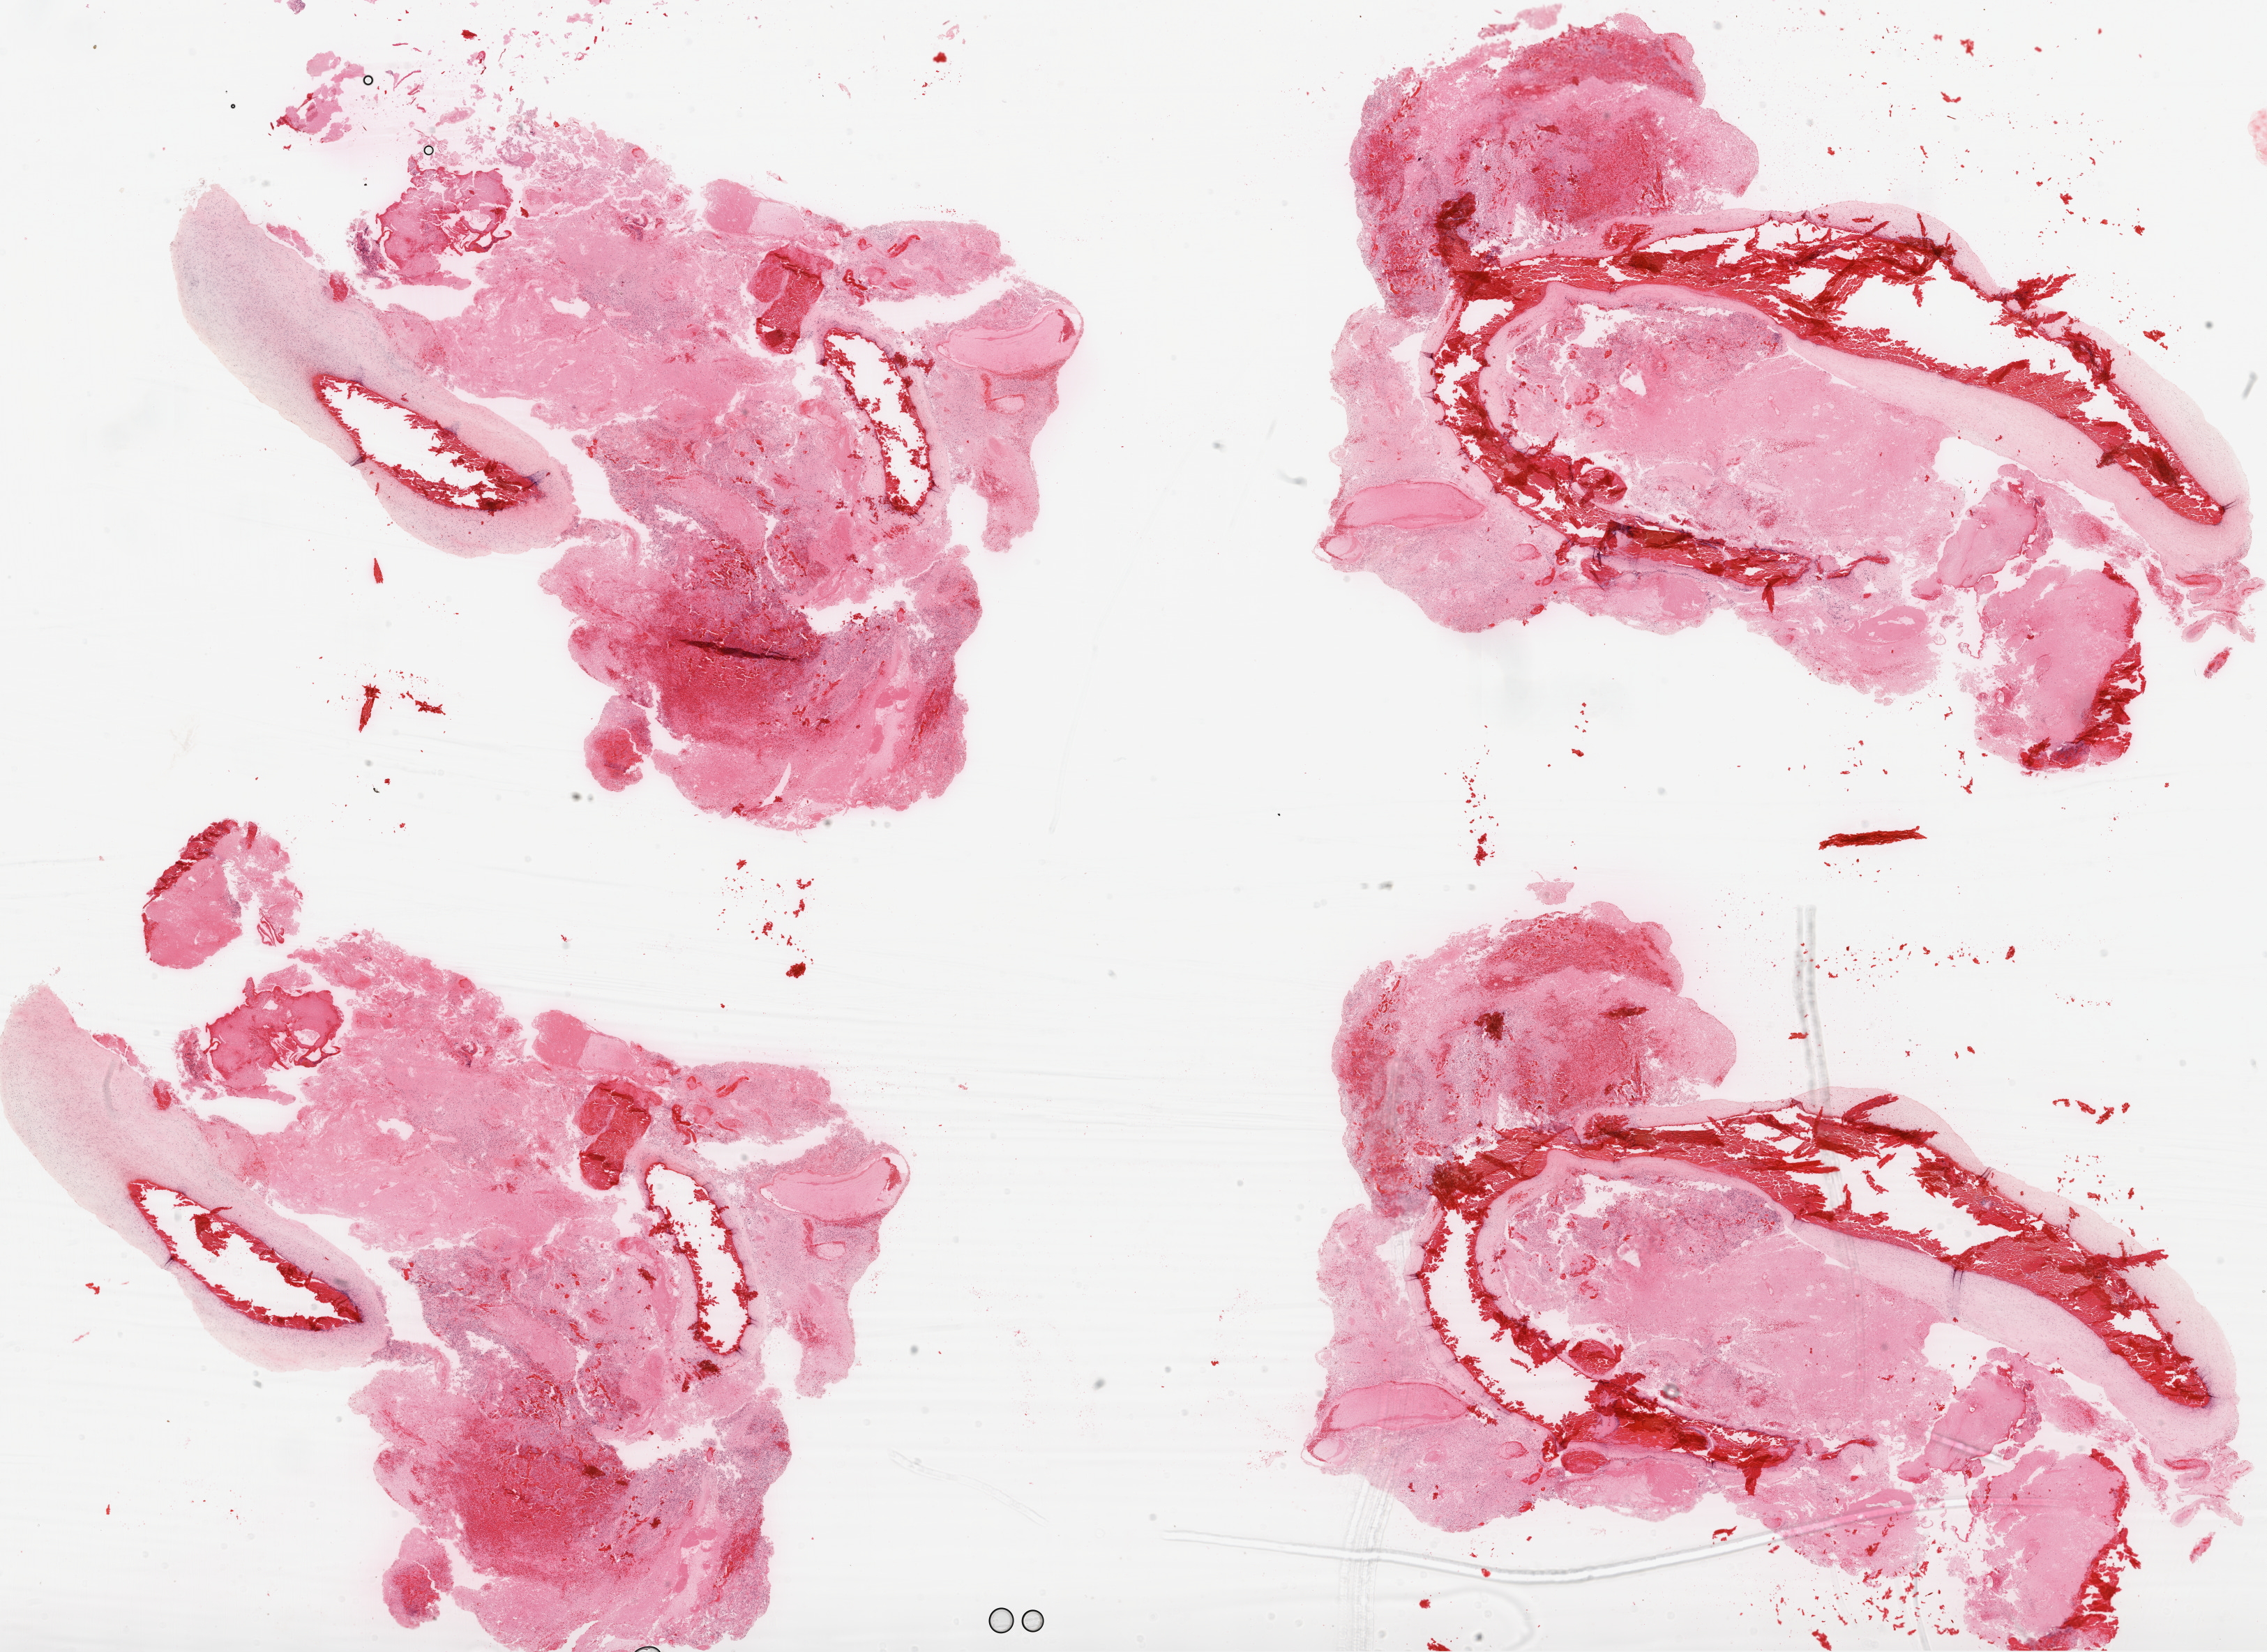
H&E whole-slide image — low-resolution overview of the scanned area, about 26.1 x 19.0 mm; formalin-fixed paraffin-embedded (FFPE) diagnostic section; primary tumour sample from the brain. Female, age 50 years at initial diagnosis.
Diagnosis: Glioblastoma.